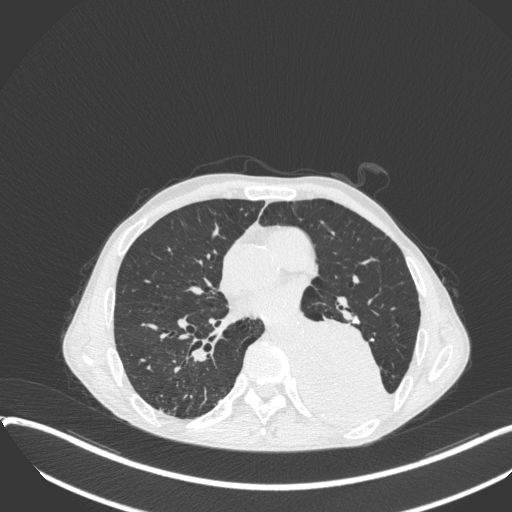
Chest CT, one axial slice; slice 172 of 400 in the series (ordered by position); 120 kVp; lung window (W 1500 / L -600 HU); 1 mm slice thickness; 512 × 512 image matrix, field of view 400 × 400 mm. Male patient, age 57 years. From the clinical record (not read from this slice): clinical TNM (as recorded): T4 N0 M0.
Structures marked on this image (bounding box drawn by a radiologist):
- lung tumour (recorded histology: squamous cell carcinoma): bounding box [x1, y1, x2, y2] px = [298, 314, 397, 431]